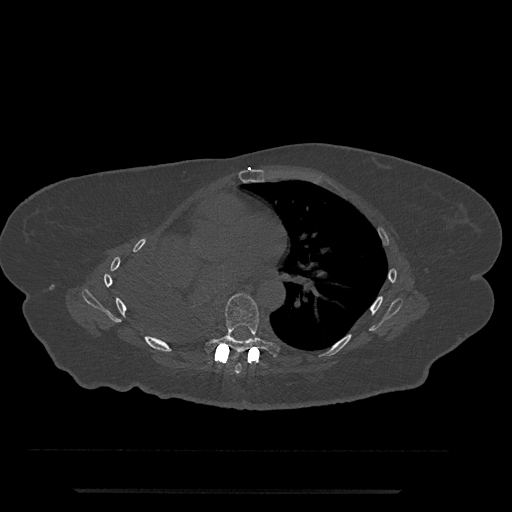
CT including the spine, one axial slice; position 447 of 797 along the scan axis; reconstruction kernel Br40s/3; 120 kVp; bone window (W 1800 / L 400 HU); 0.5 mm slice thickness; 512 × 512 image matrix, field of view 440 × 440 mm. Patient: female, 51 years. Case-level facts recorded for this patient, not image findings: primary cancer: neuro.
Outlined on this slice (semi-automatic segmentation, software-assisted and operator-edited):
- T6 vertebra: bounding box (x1, y1, x2, y2) in pixels: (234, 363, 242, 374)
- T7 vertebra: (205, 293, 281, 356)